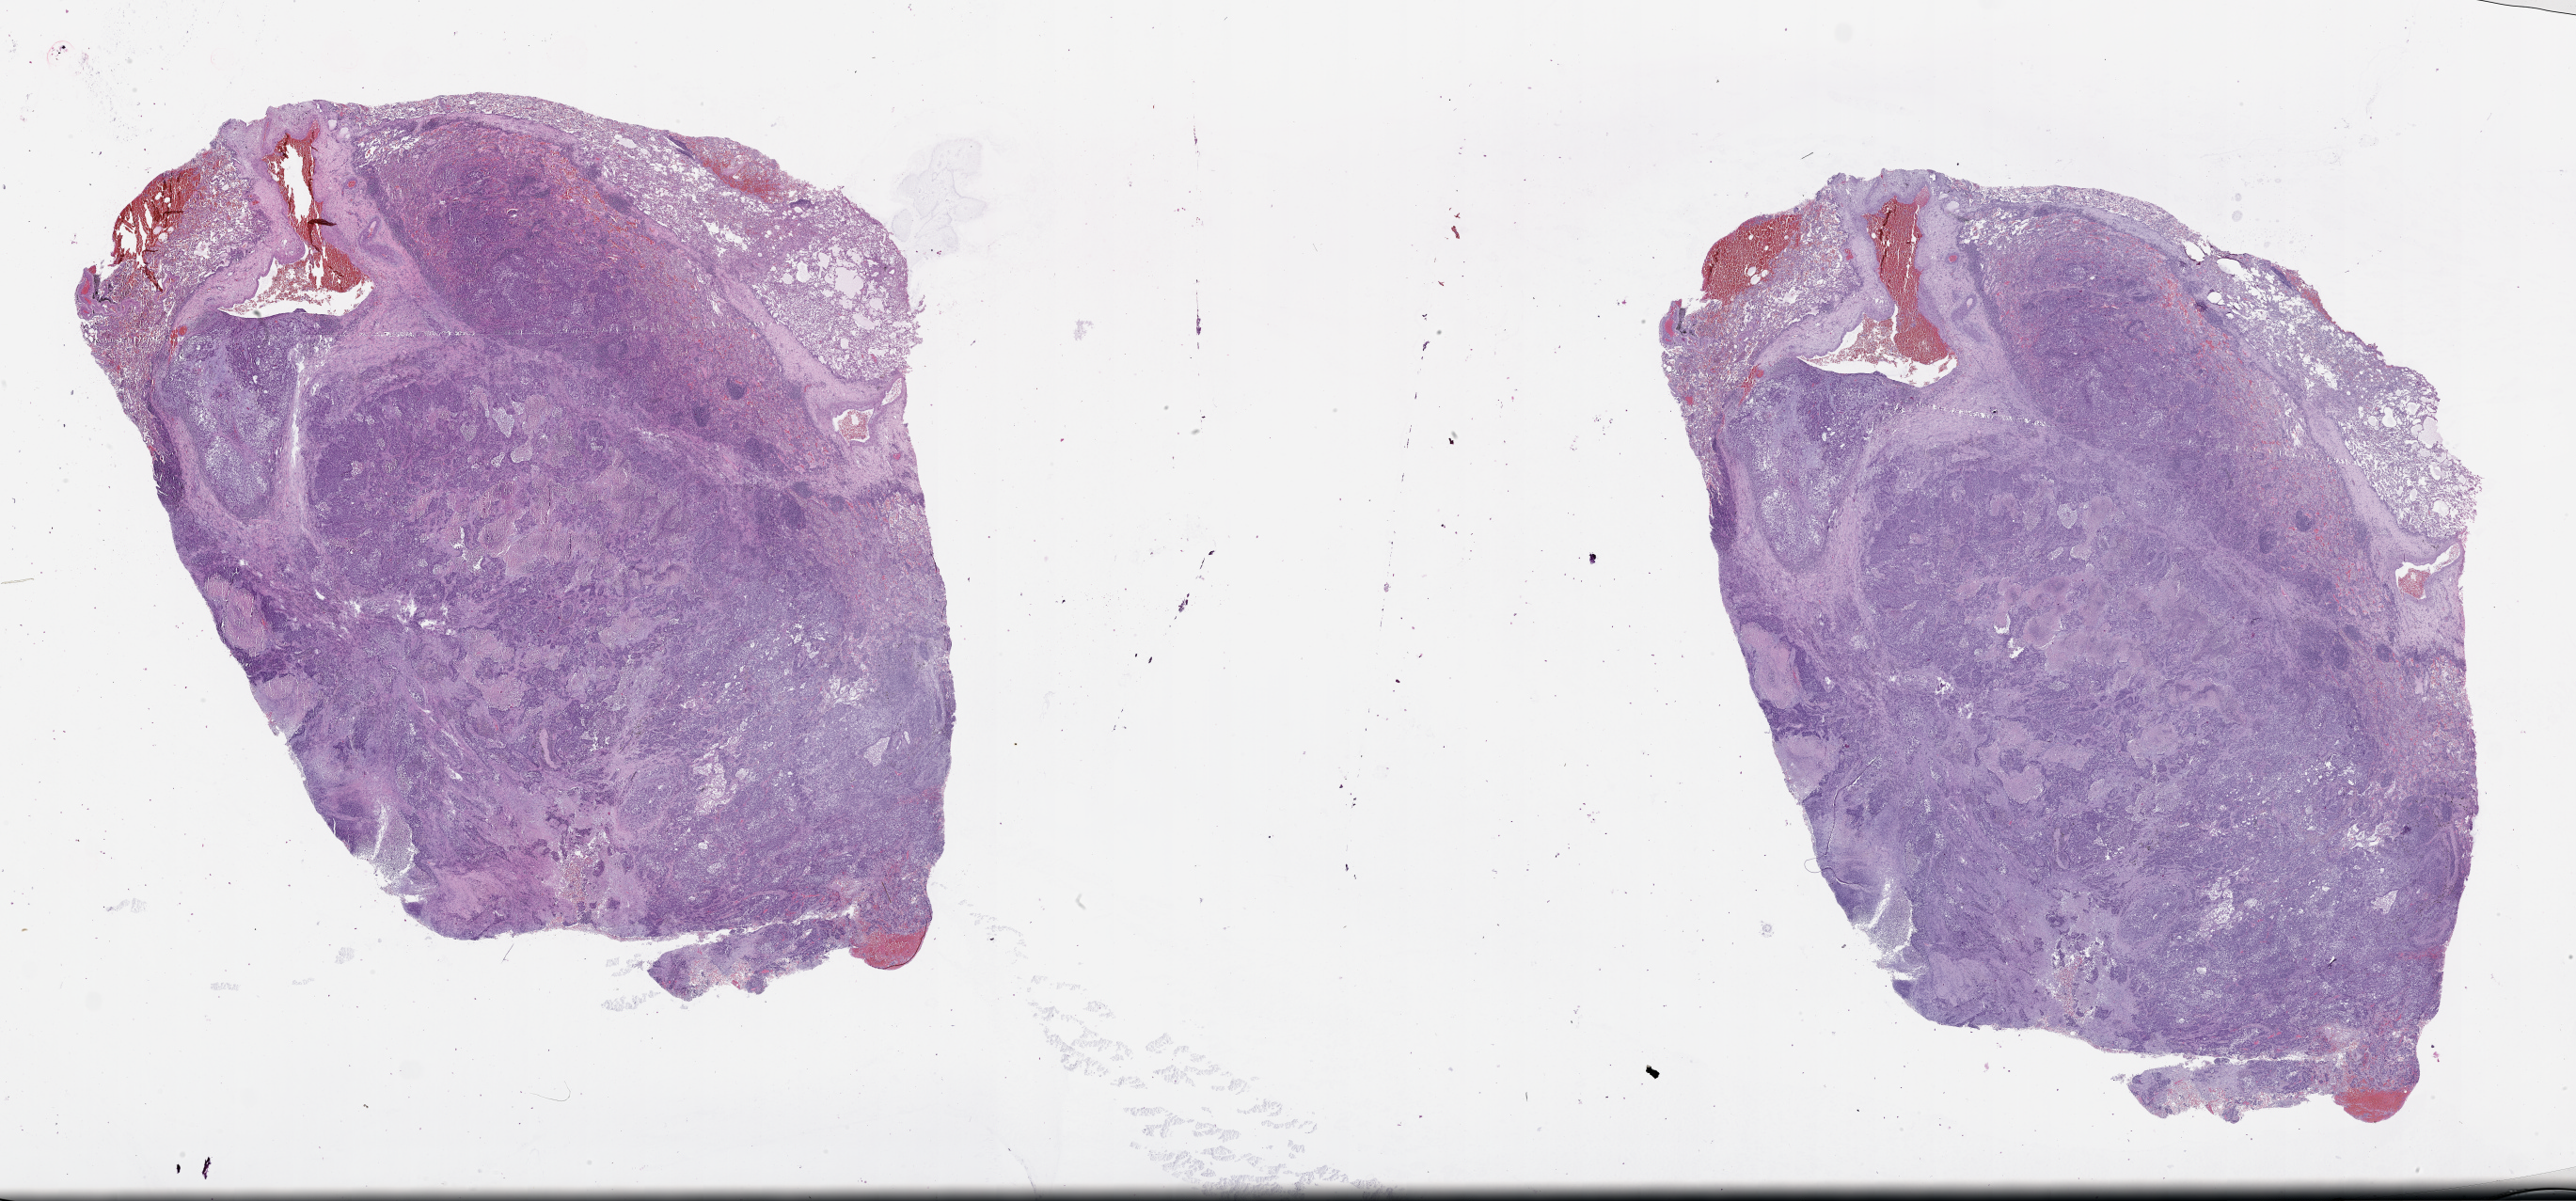
Digitized Hematoxylin and eosin (H&E) stained tissue section (whole slide), a low-resolution overview of the entire scanned area, about 44.1 x 20.6 mm (from a 20x scan). Lung, tissue type not recorded.
- patient diagnosis (cohort enrolment): squamous cell carcinoma (lung)